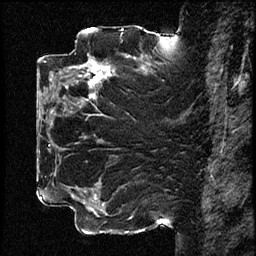
Breast MRI (dynamic contrast-enhanced), one sagittal slice. Position 39 of 78 along the scan axis. Dynamic contrast-enhanced study with each time point stored as its own series, time point 2 of 3 at this slice position (early post-contrast, ordered by acquisition time). 1.5 T. TE 4.2 ms, TR 17.6 ms. 256 × 256 image matrix. Female patient, age 42 years. From the clinical record (not read from this slice): setting: breast cancer imaged before/during neoadjuvant chemotherapy; receptor status: HER2-positive.
Outlined on this slice (semi-automatically segmented with operator editing):
- analysis volume of interest (the breast-tissue region the enhancement analysis was run in; not a lesion): box from (x=50, y=48) to (x=130, y=129) px
- tumour enhancement mask (voxels above the 100 % enhancement threshold inside the analysis volume of interest): (x=66, y=59)–(x=111, y=97)